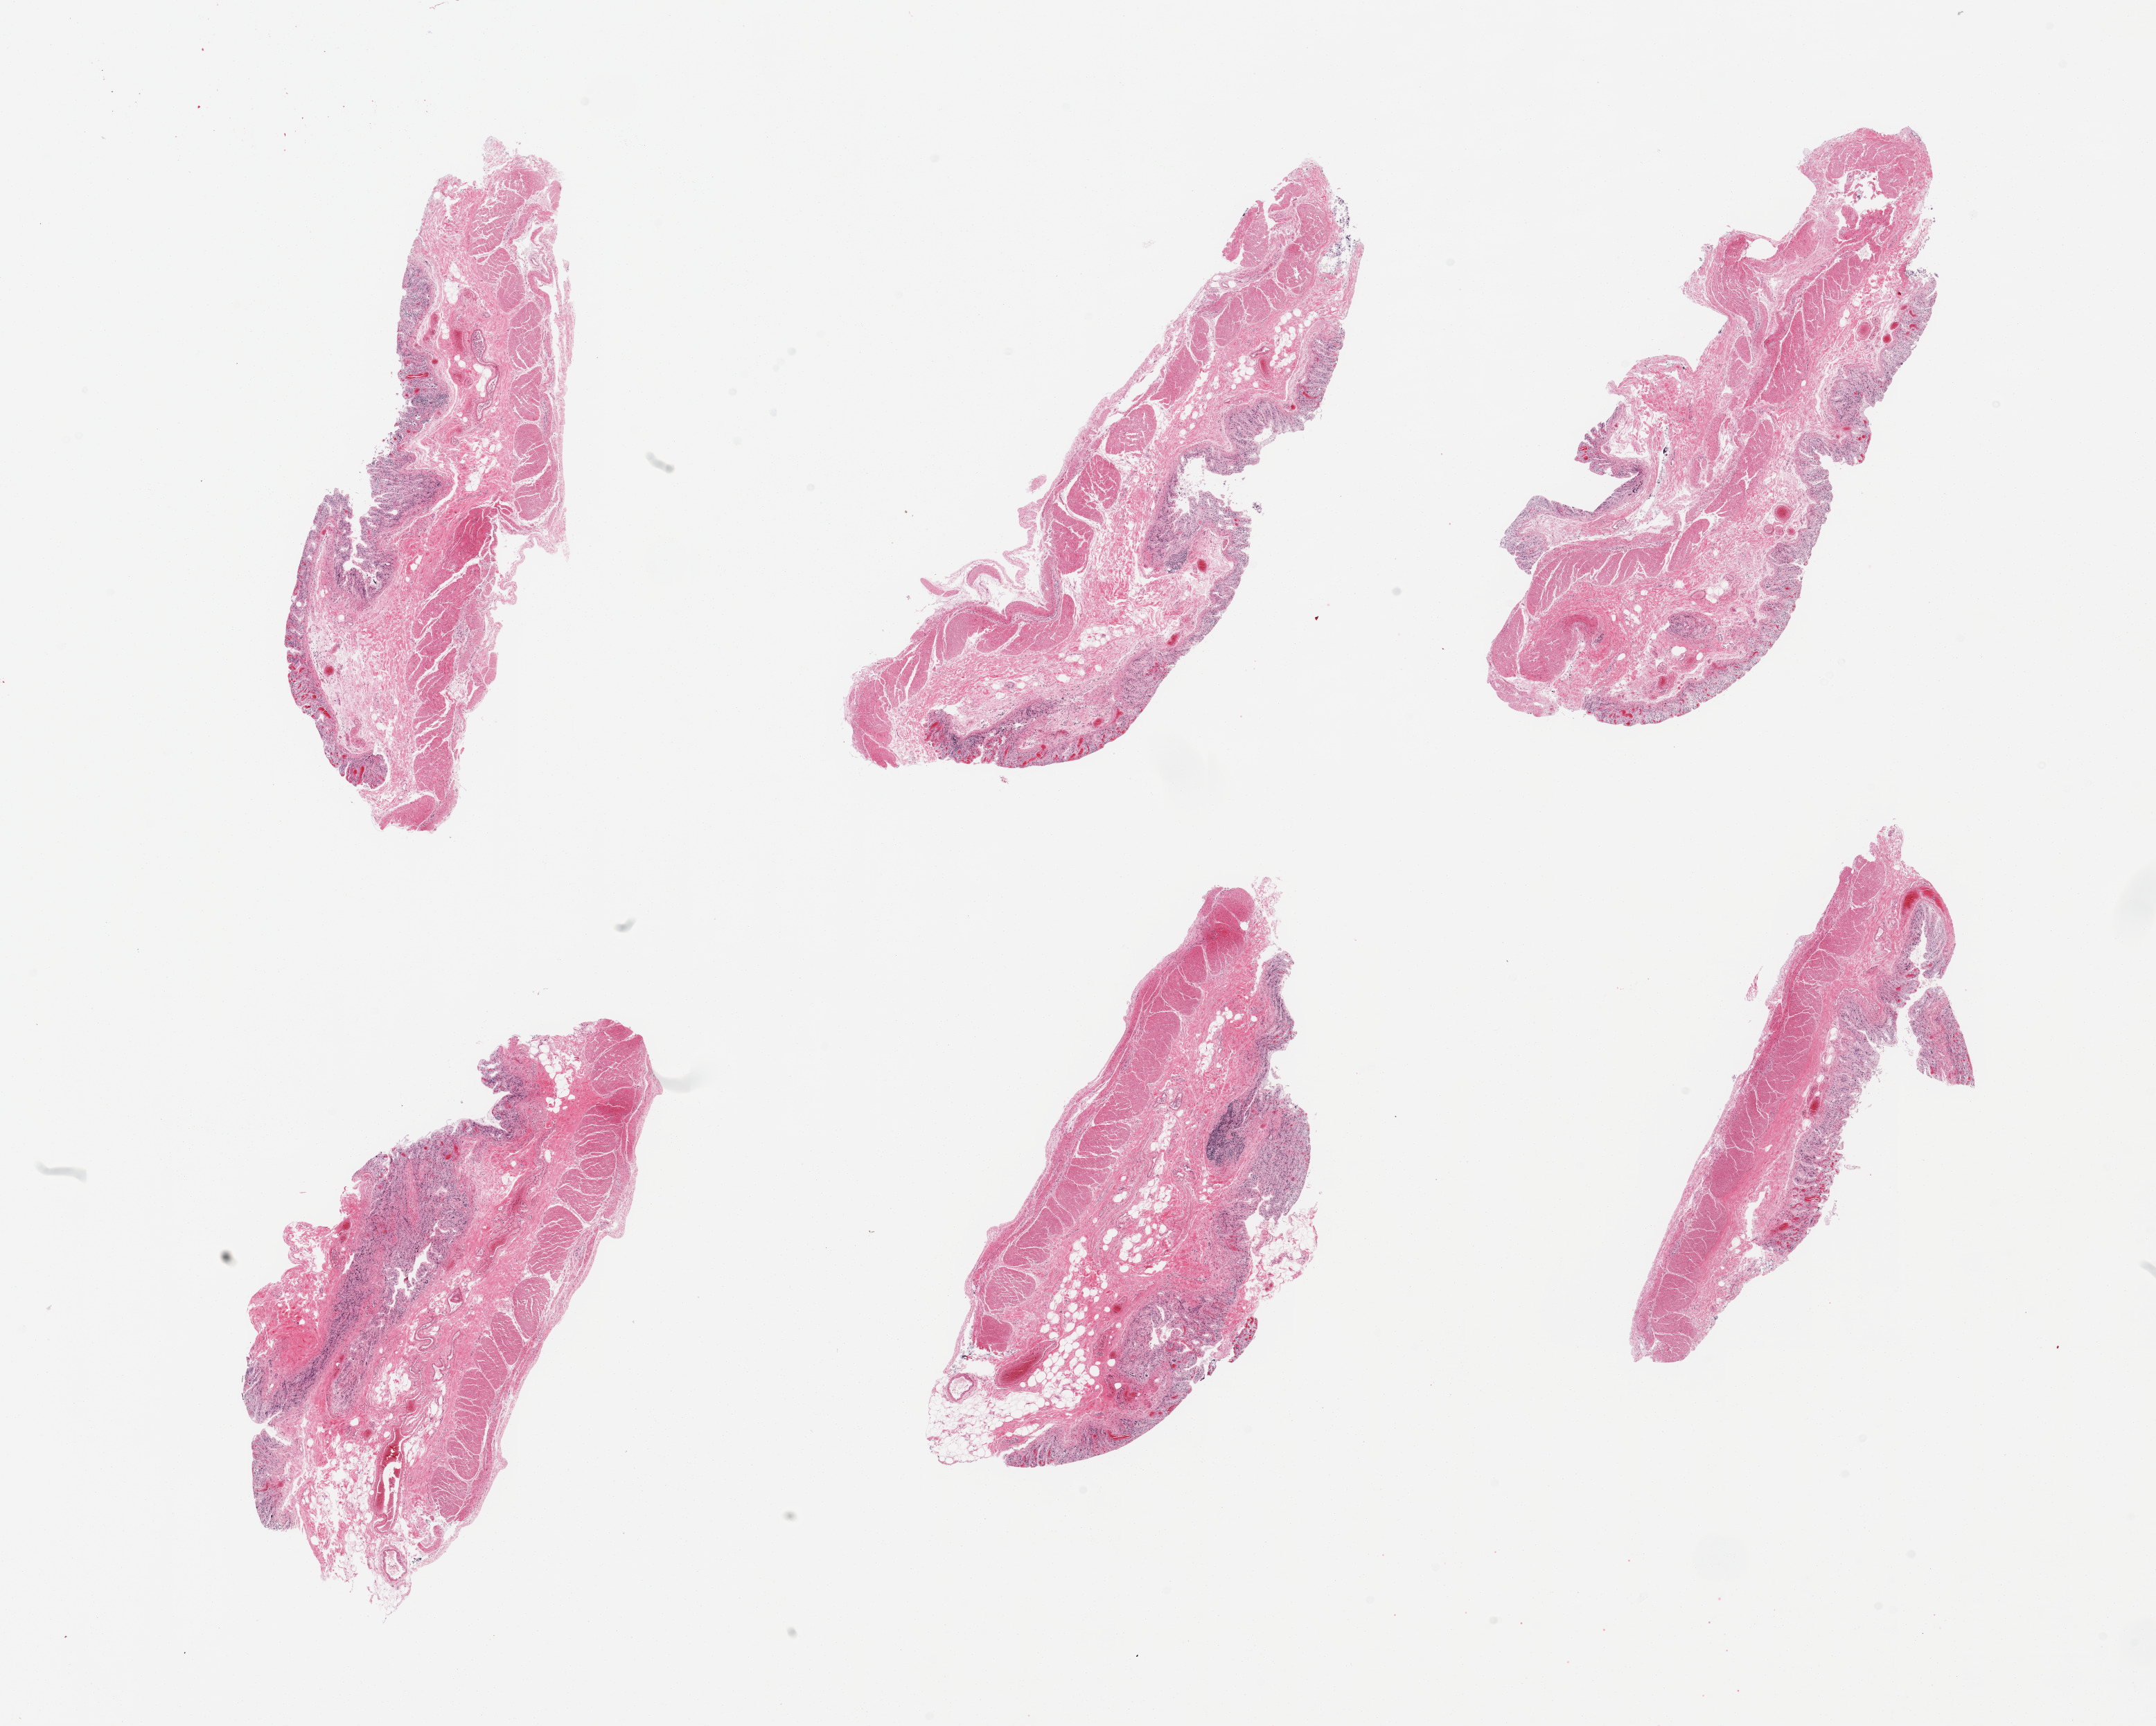
Whole-slide image, H&E stain — low-resolution overview of the scanned area, about 24.6 x 19.7 mm. PAXgene-fixed paraffin-embedded (PFPE) section. Section of transverse colon (target tissue). Donor tissue sample. Donor sex: male.
Review note (as recorded): 6 pieces, mucosa with advanced autolysis/sloughing.